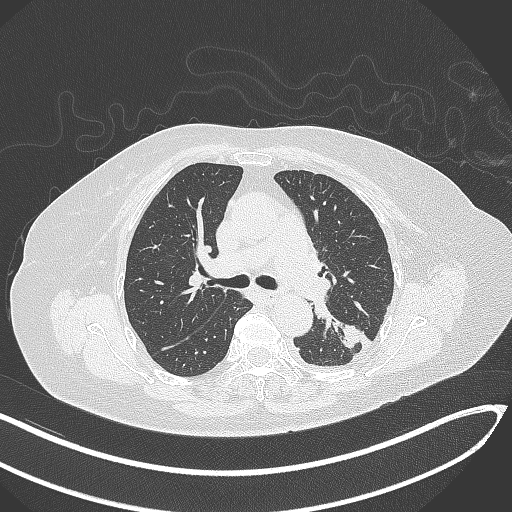
Chest CT, one axial slice; position 200 of 270 along the scan axis; reconstruction kernel B70f; 120 kVp; lung window (W 1500 / L -600 HU); 1 mm slice thickness; 512 × 512 image matrix, field of view 400 × 400 mm. Female patient, age 76 years. From the clinical record (not read from this slice): clinical TNM (as recorded): T1c N0 M0.
Annotated regions visible in this slice (bounding box drawn by a radiologist):
- lung tumour (recorded histology: adenocarcinoma): box from (x=338, y=320) to (x=358, y=352) px